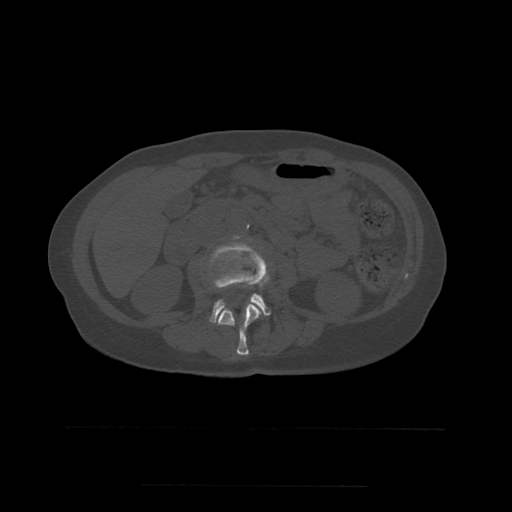
CT including the spine, one axial slice; position 200 of 544 along the scan axis; bone window (W 1800 / L 400 HU); 512 × 512 image matrix, field of view 350 × 350 mm. Patient age 58 years. Case-level facts recorded for this patient, not image findings: primary cancer: lung.
Annotated regions visible in this slice (semi-automatically segmented with operator editing):
- L2 vertebra: box from (x=216, y=237) to (x=266, y=356) px
- L3 vertebra: (x=210, y=237)–(x=271, y=323)